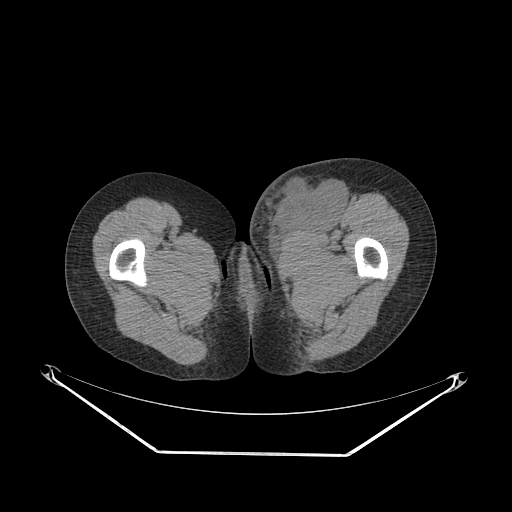
CT of an extremity soft-tissue mass (from a PET/CT study), one axial slice; reconstruction kernel SOFT; 140 kVp; soft-tissue window (W 400 / L 40 HU); 3.75 mm slice thickness; 512 × 512 image matrix, field of view 500 × 500 mm. Female patient. From the clinical record (not read from this slice): histological type: leiomyosarcoma; grade: high; site of the primary tumour: groin.
Outlined on this slice (expert contour drawn on MRI and transferred to this co-registered scan by the dataset authors):
- gross tumour volume including surrounding oedema: bounding box (x1, y1, x2, y2) in pixels: (249, 169, 346, 243)
- gross tumour volume (mass): (272, 181, 346, 232)